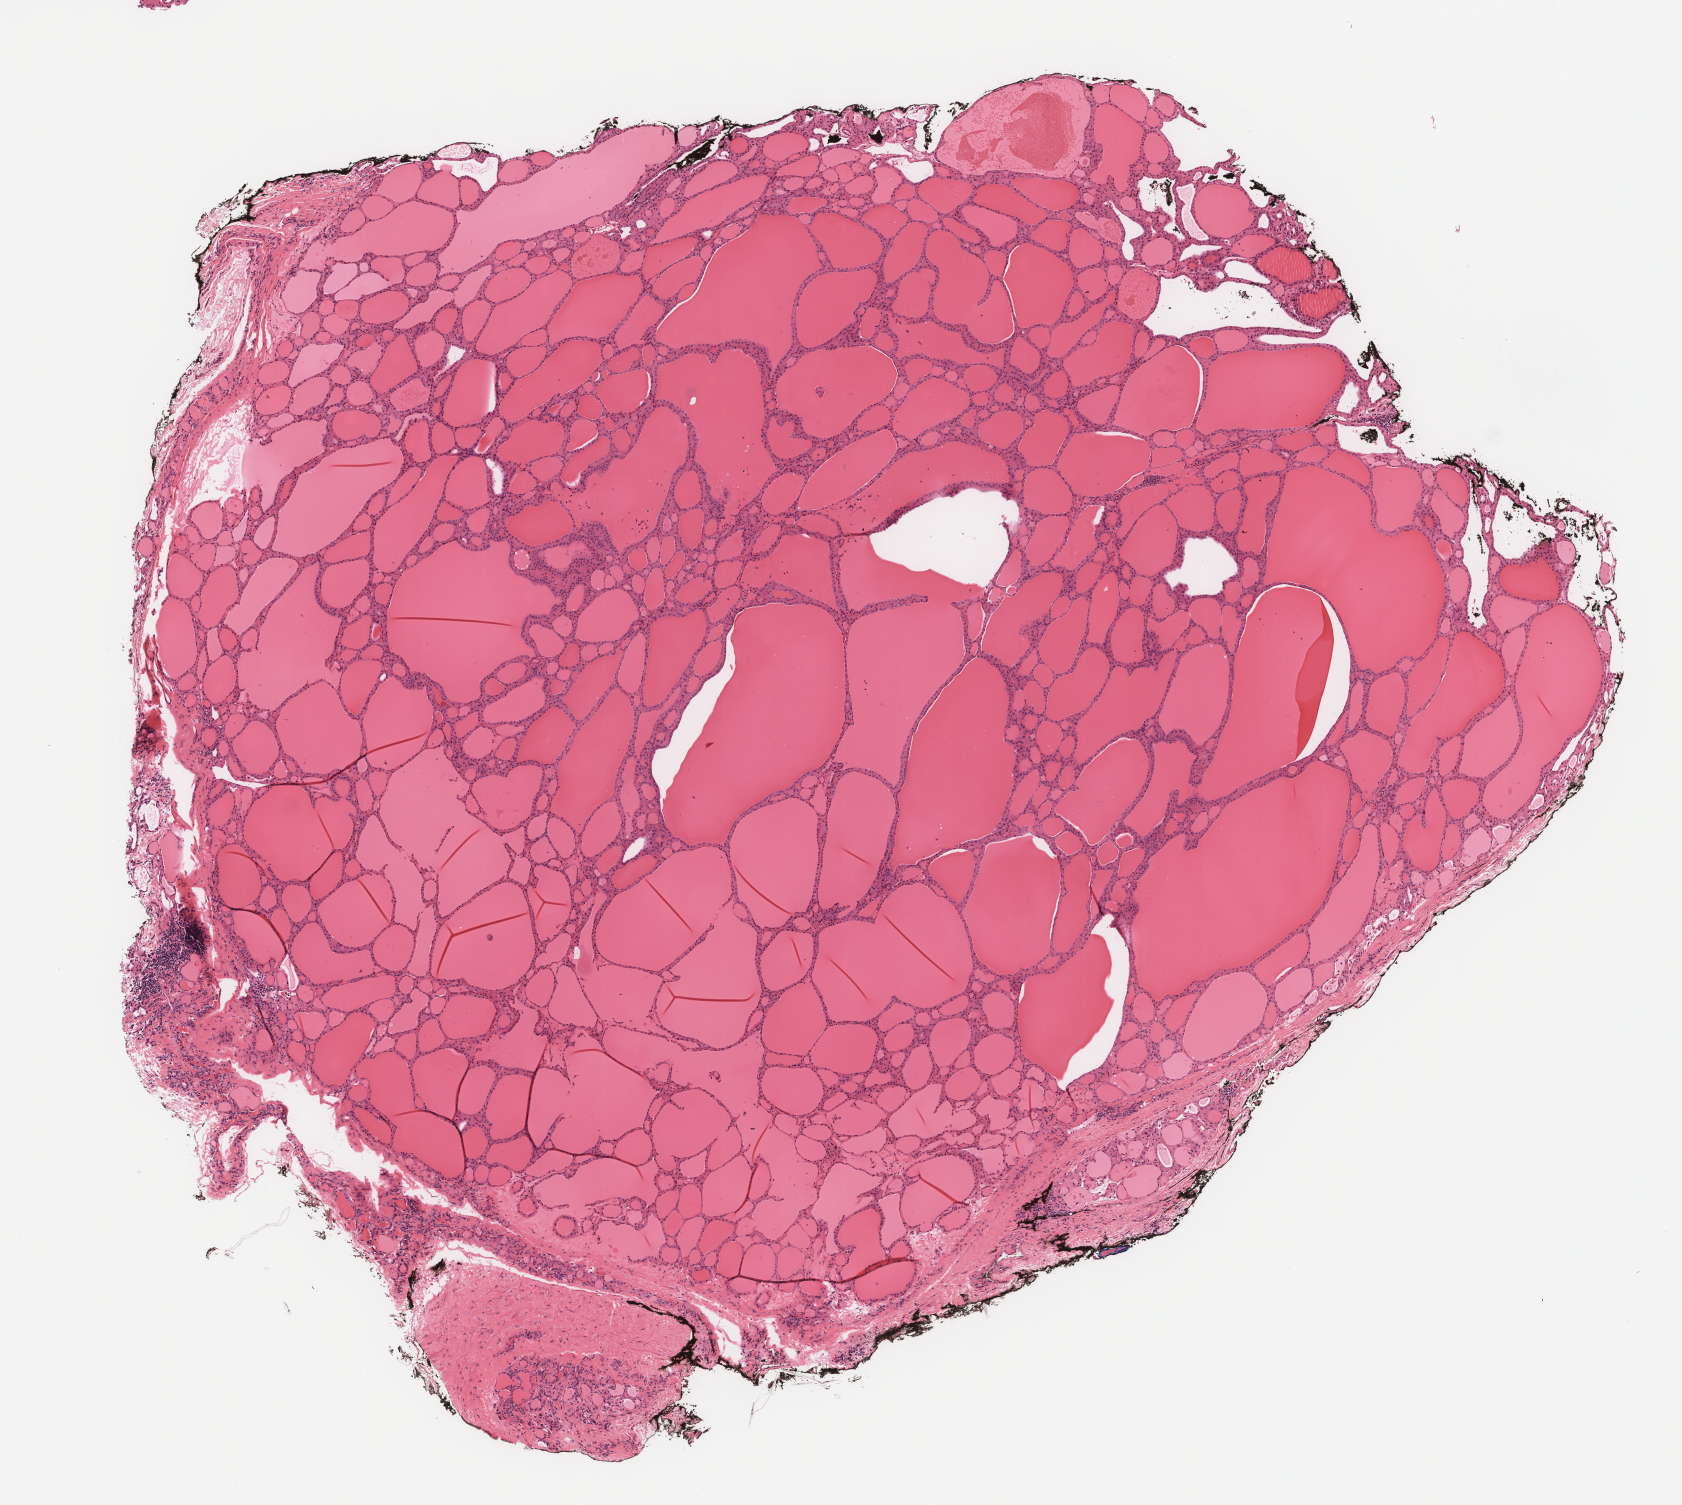
Hematoxylin and eosin (H&E) stained whole-slide image, whole scanned area (about 6.8 x 6.1 mm, acquisition: 40x scan) shown as a low-resolution overview. Formalin-fixed paraffin-embedded (FFPE) diagnostic section. Primary tumour sample from the thyroid. Female, age 63 years at initial diagnosis.
Pathologic diagnosis: Papillary carcinoma, follicular variant (thyroid gland).